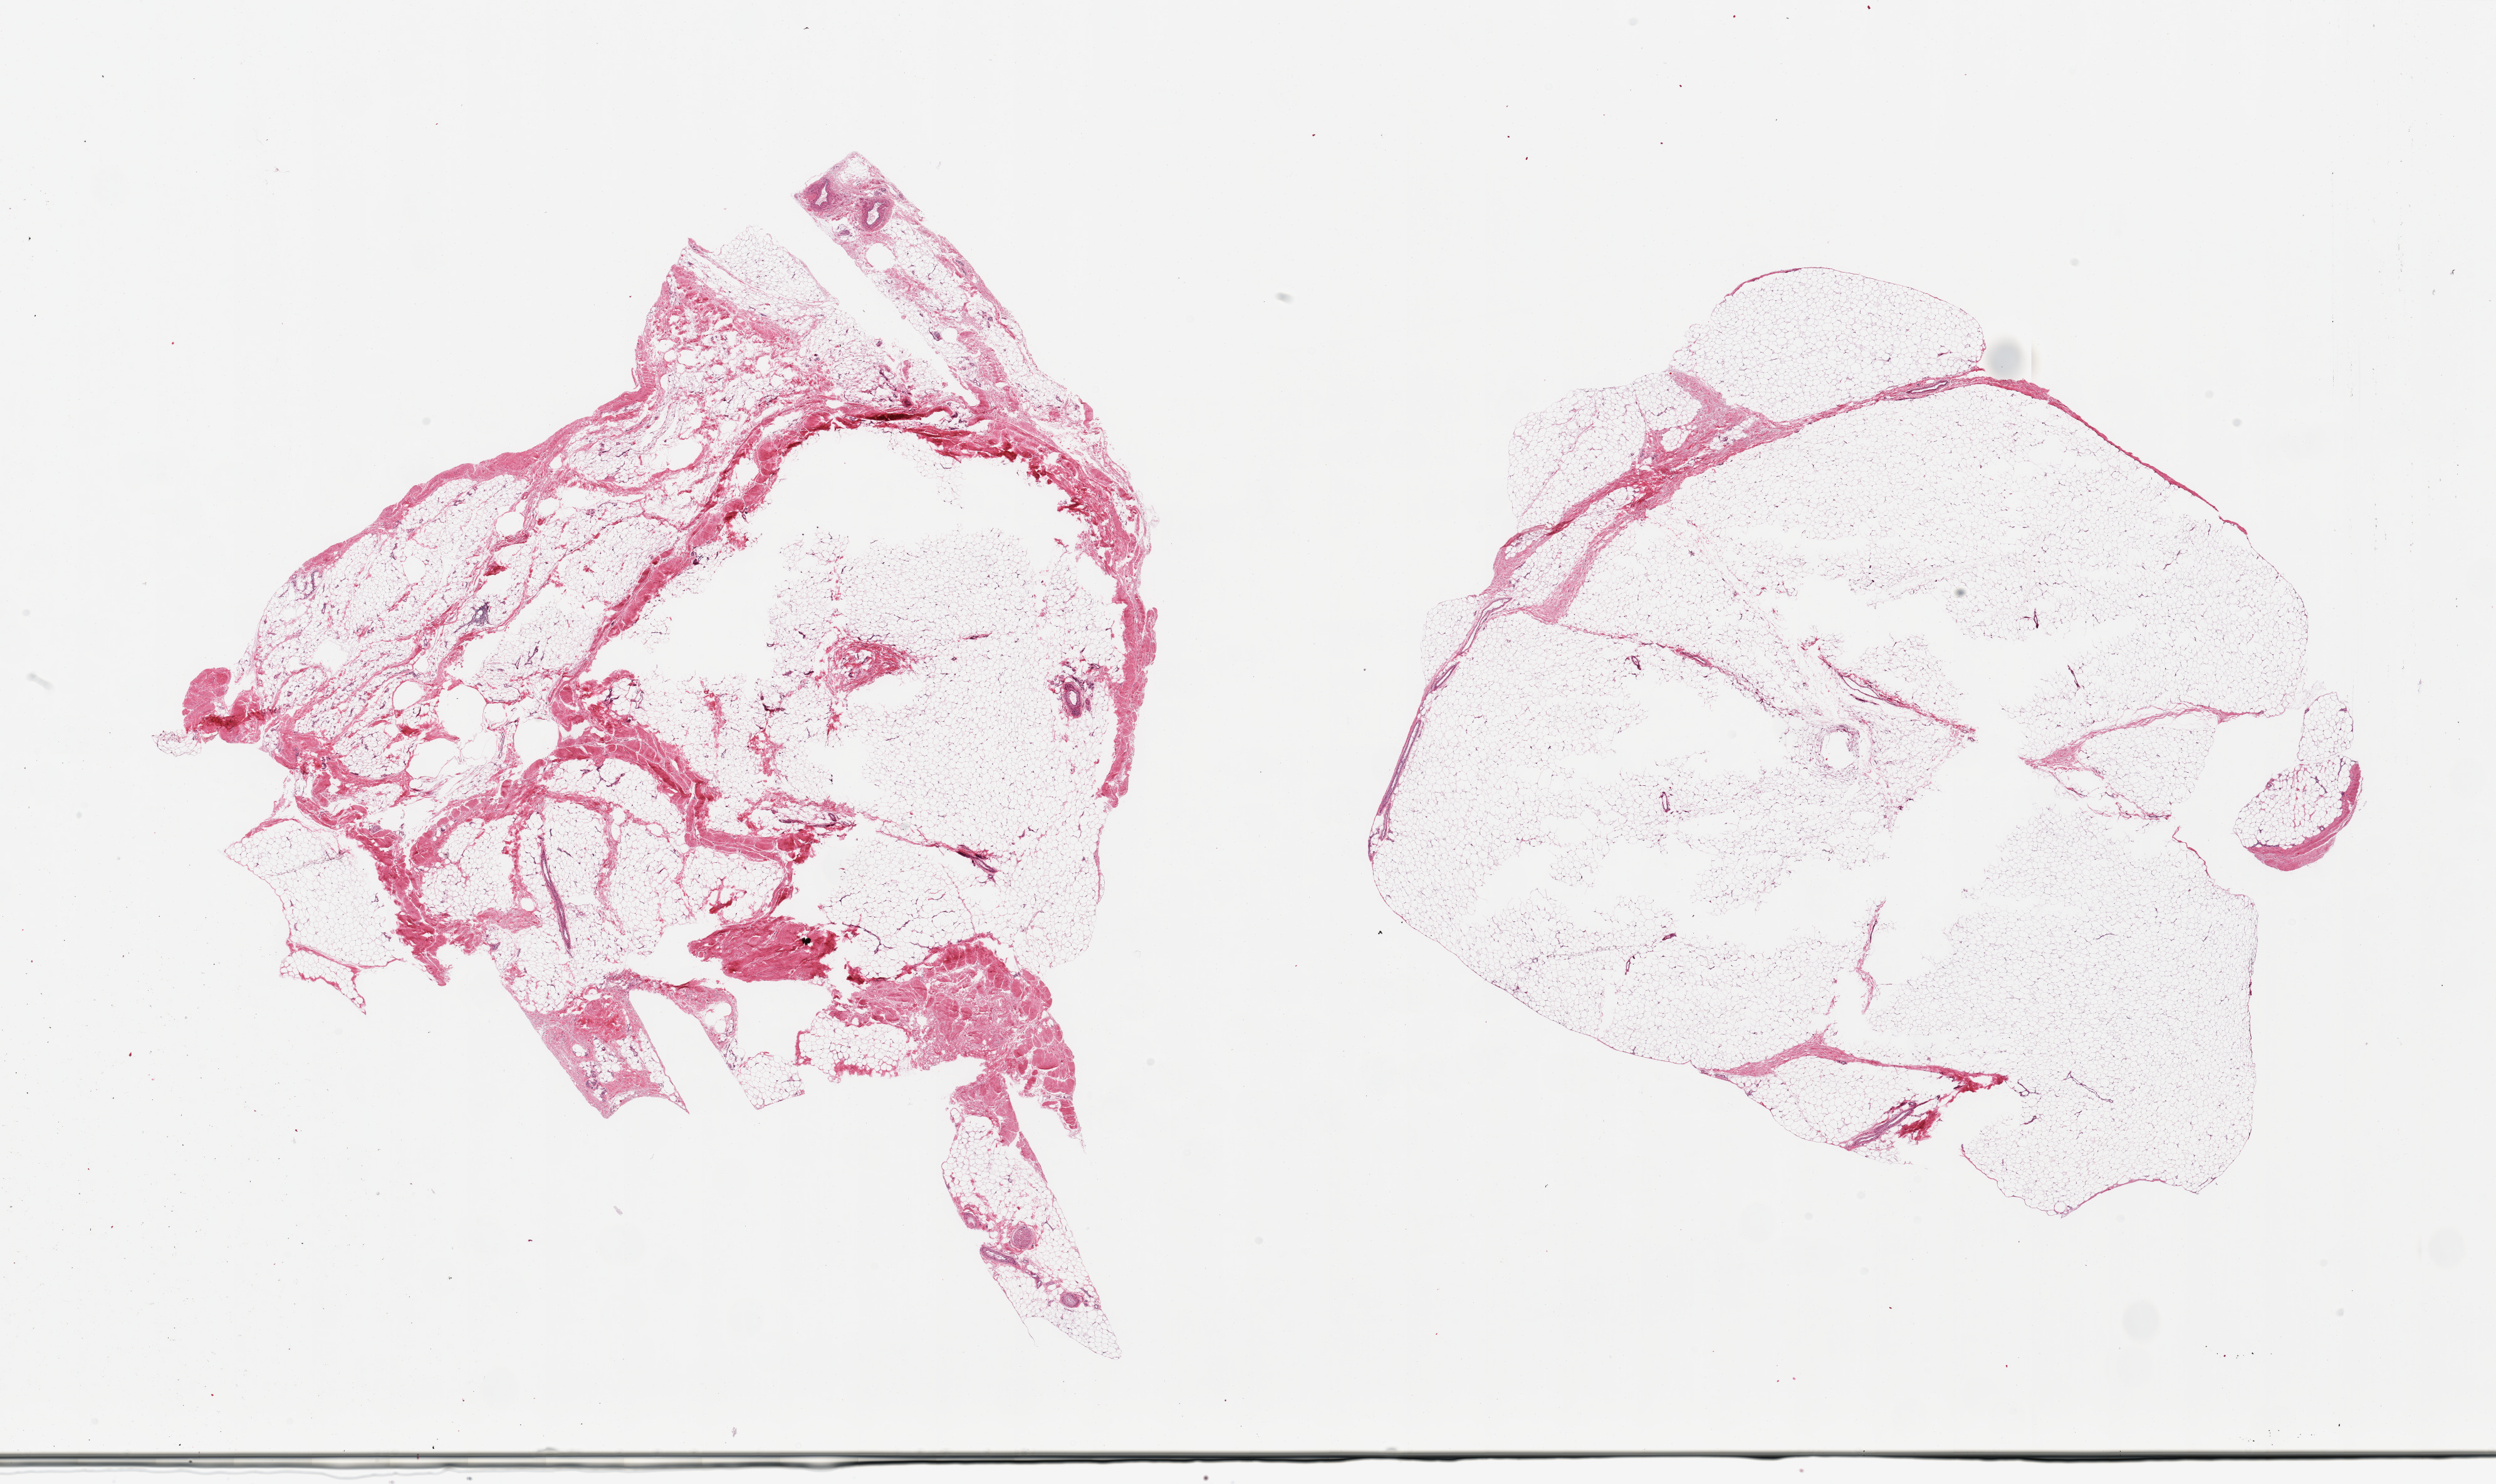
Hematoxylin and eosin (H&E) whole-slide image — a low-resolution overview of the entire scanned area, about 31.5 x 18.7 mm. PAXgene-fixed, paraffin-embedded tissue. Sampled site (target tissue): adipose tissue. Tissue donor sample. Male donor.
• pathologist's review note for this sample: 2 pieces; central defects, mature fat with 5 and 40% fibrocollagenous tissue/tendon/vessels/nerve